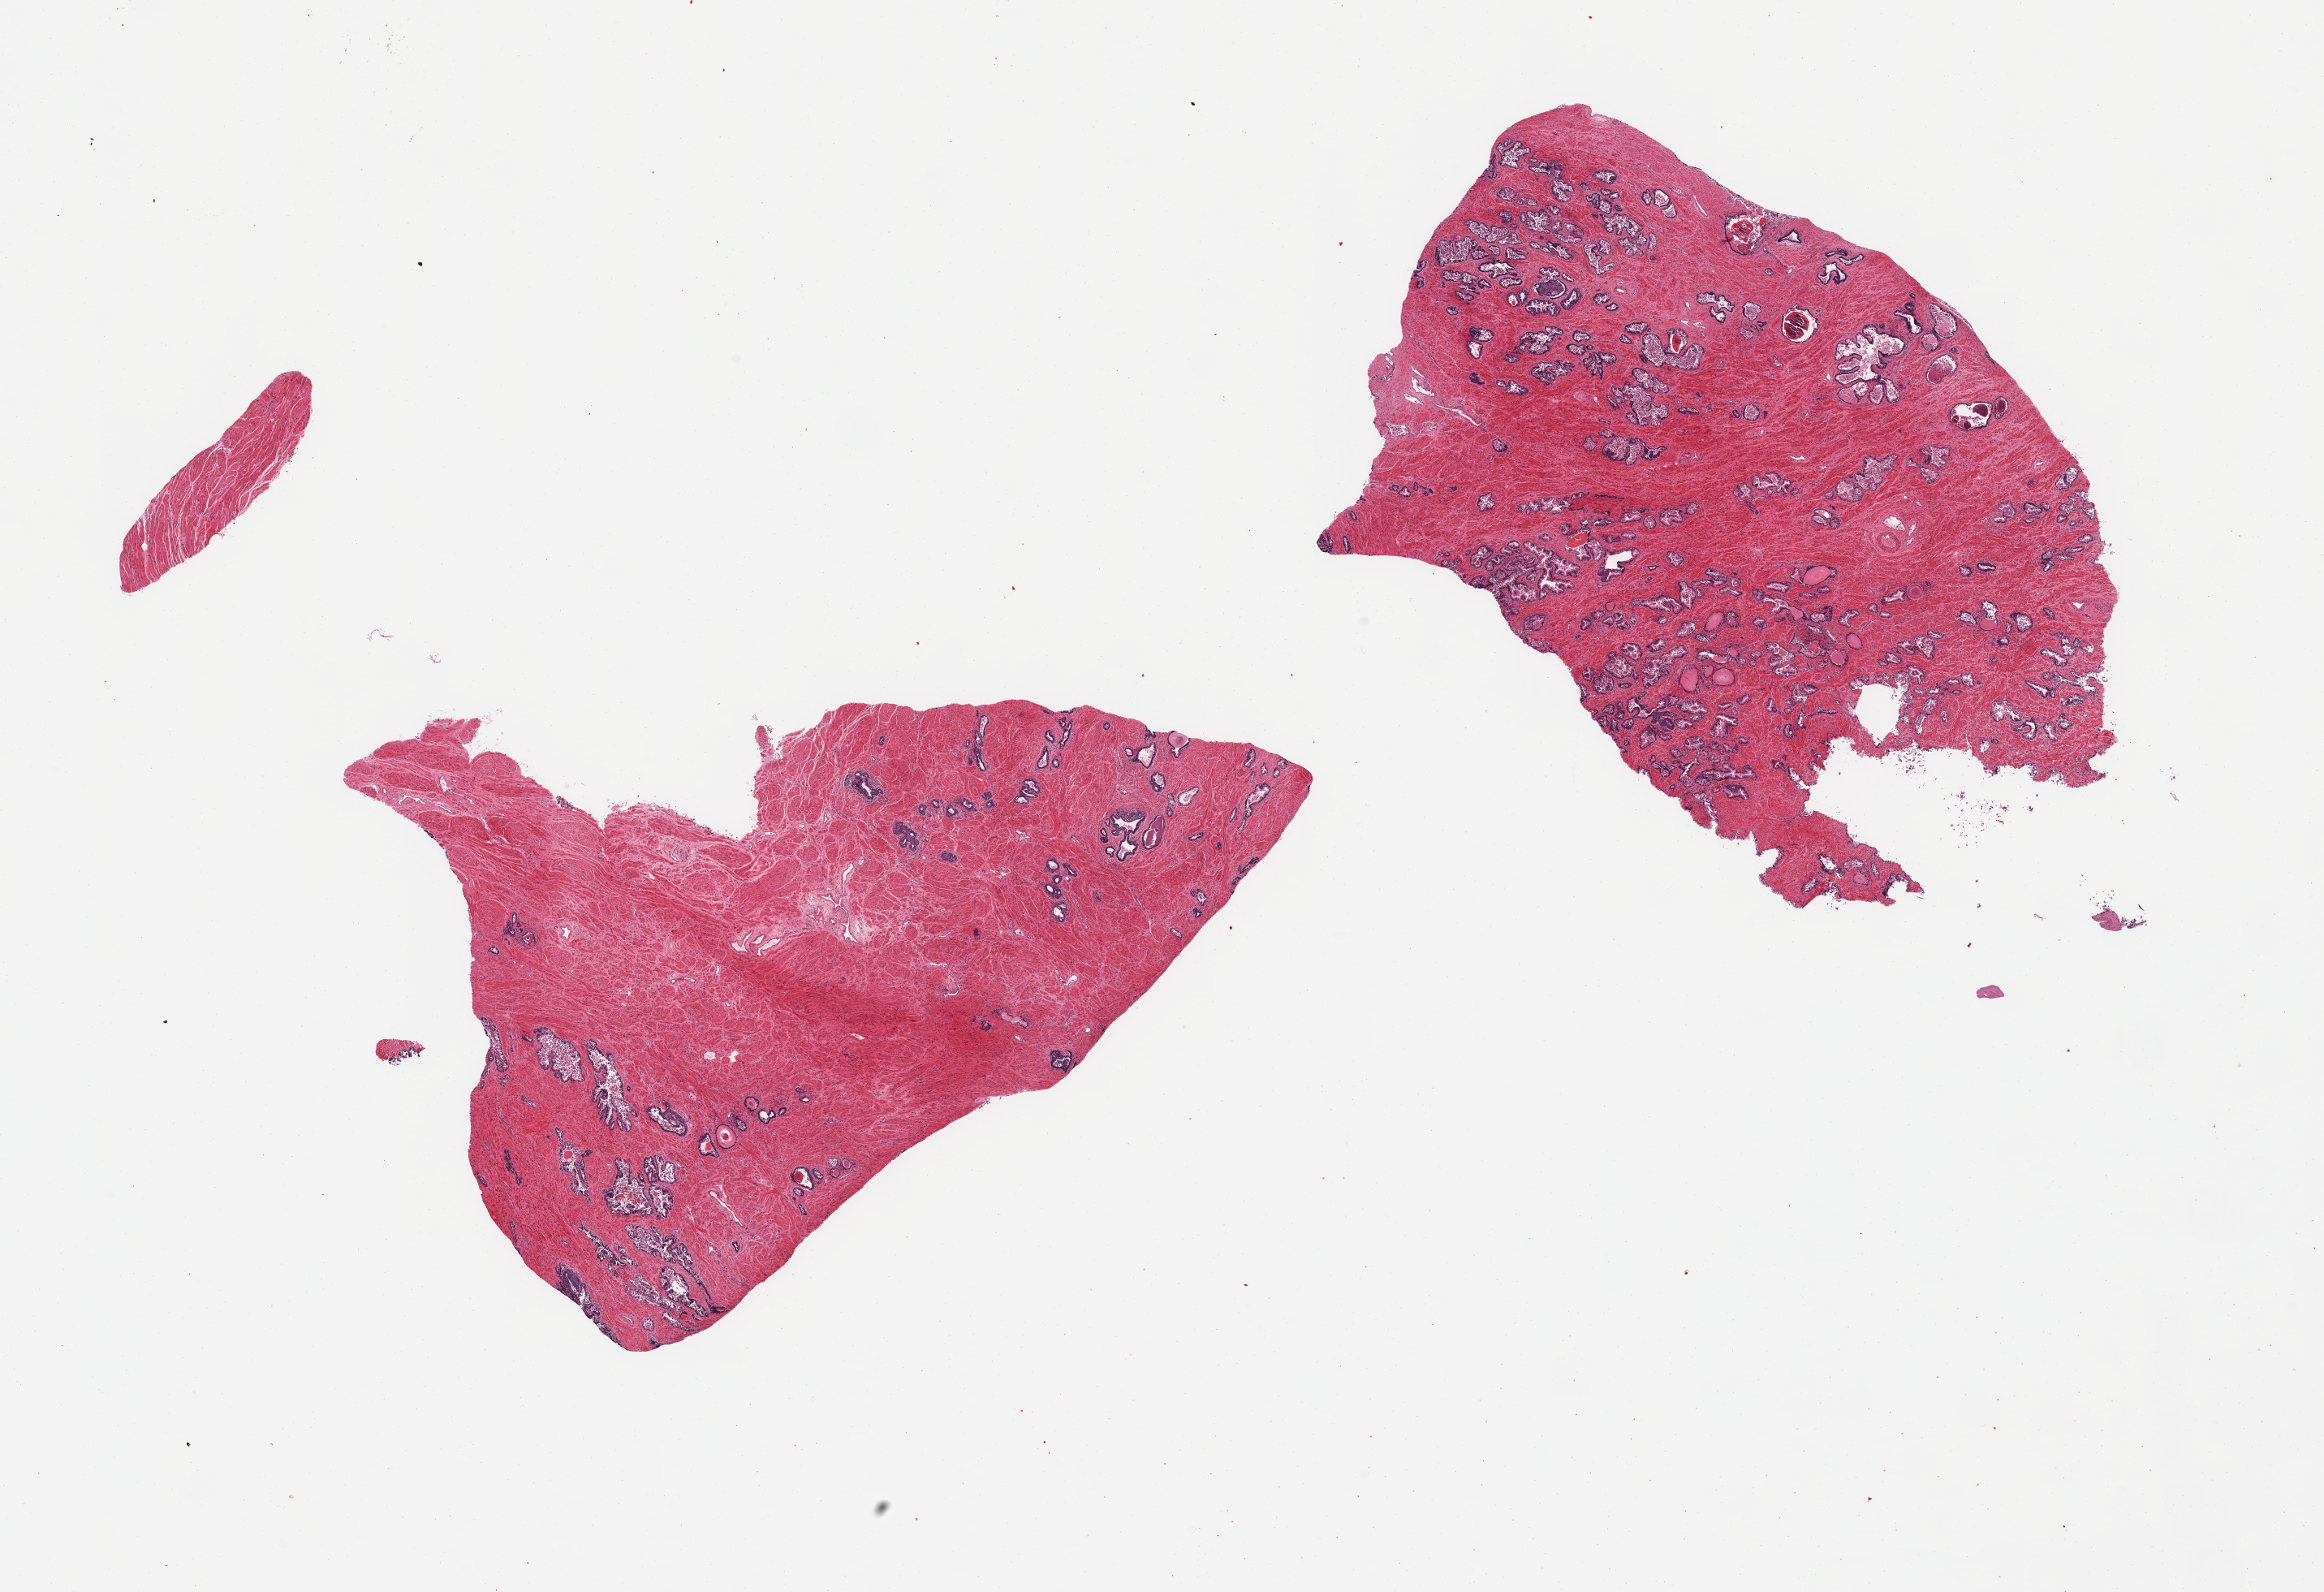
Digitized hematoxylin and eosin (H&E)-stained section, brightfield, shown as a low-resolution overview of the whole scanned area (about 22.6 x 15.5 mm); PAXgene-fixed paraffin-embedded (PFPE) section; target tissue: prostate; tissue donor sample. Donor: male.
Pathologist's review note for this sample: 2 pieces; fibromuscular stroma and glands with partially sloughed lining, several corpora amylacea.